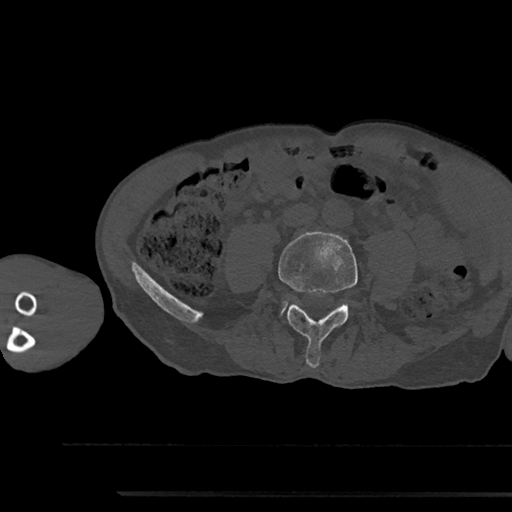
CT including the spine, one axial slice. Position 400 of 797 along the scan axis. Reconstruction kernel Br40s/3. Bone window (W 1800 / L 400 HU). 0.5 mm slice thickness. 512 × 512 image matrix, field of view 367 × 367 mm. Male patient, age 79 years. From the clinical record (not read from this slice): primary cancer: prostate.
Structures marked on this image (semi-automatically segmented with operator editing):
- L4 vertebra: bounding box [x1, y1, x2, y2] px = [278, 231, 358, 368]